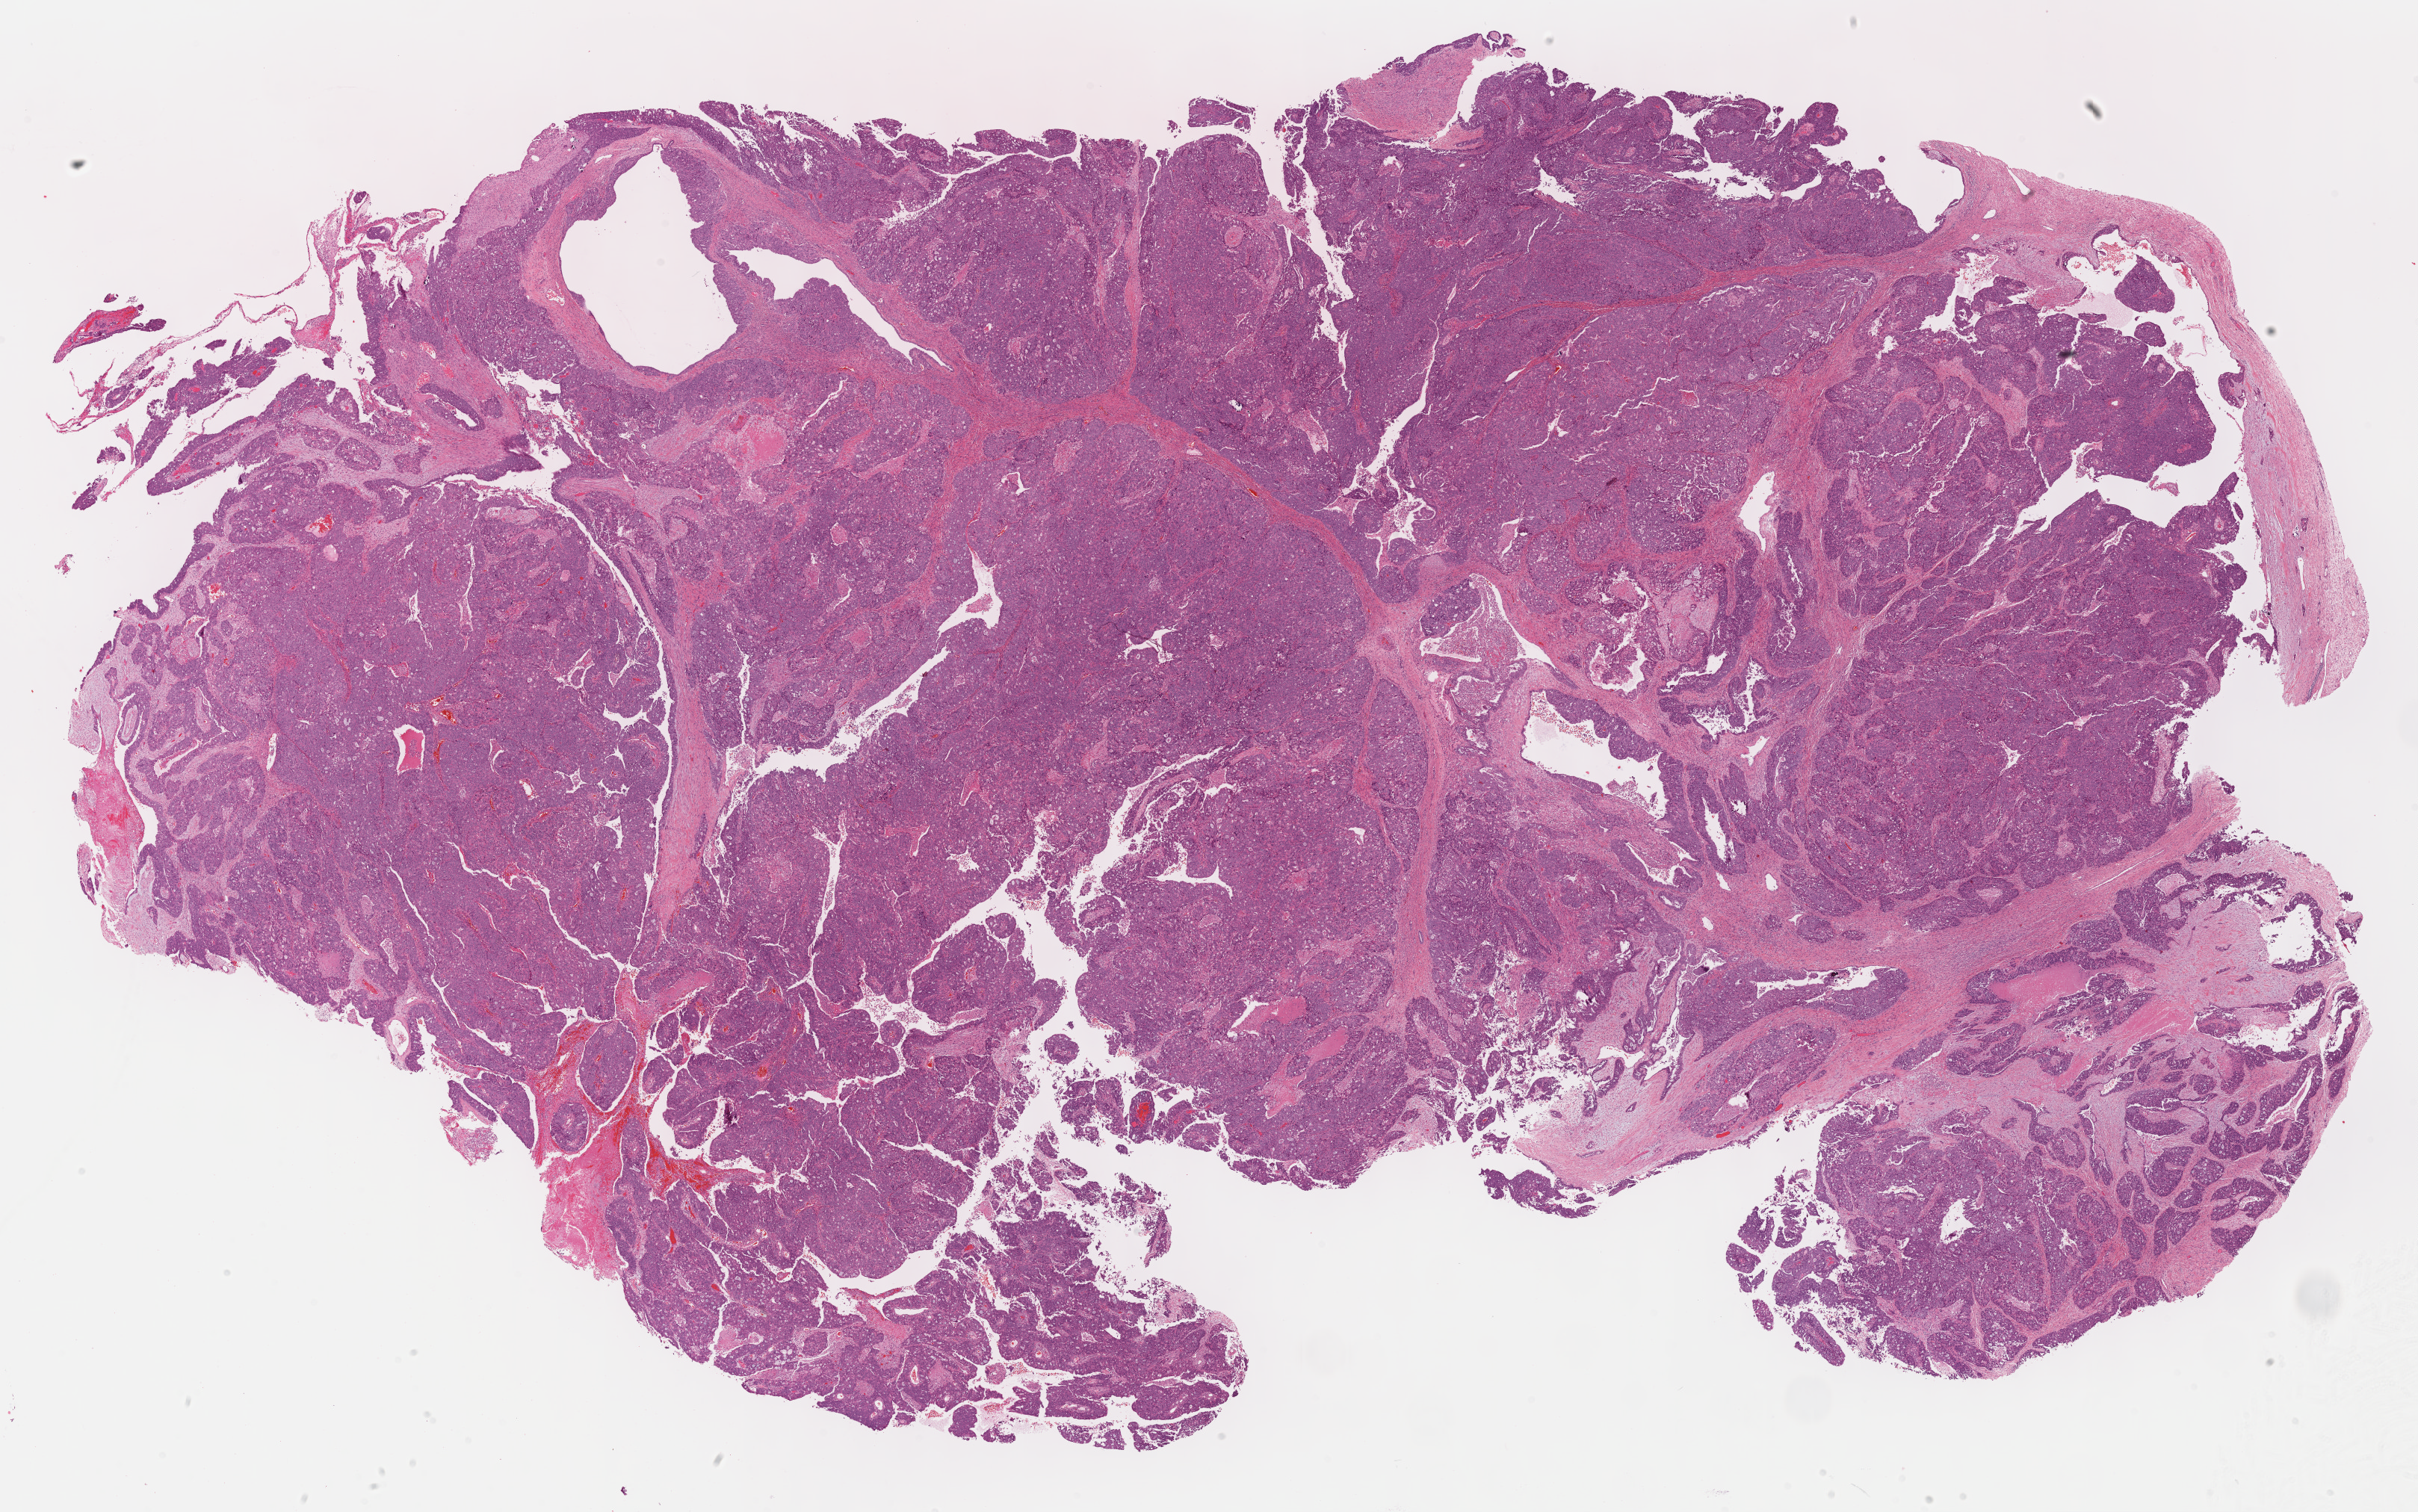
Whole-slide histology image, Hematoxylin and eosin (H&E) stained — shown as a low-resolution overview of the whole scanned area (about 26.2 x 16.4 mm), formalin-fixed paraffin-embedded (FFPE) diagnostic section, primary tumour sample from the ovary. Female patient; age at initial diagnosis 45 years. Histologic grade: G3 (poorly differentiated).
• histologic diagnosis: Serous cystadenocarcinoma, NOS
• laterality: right
• FIGO stage: IV